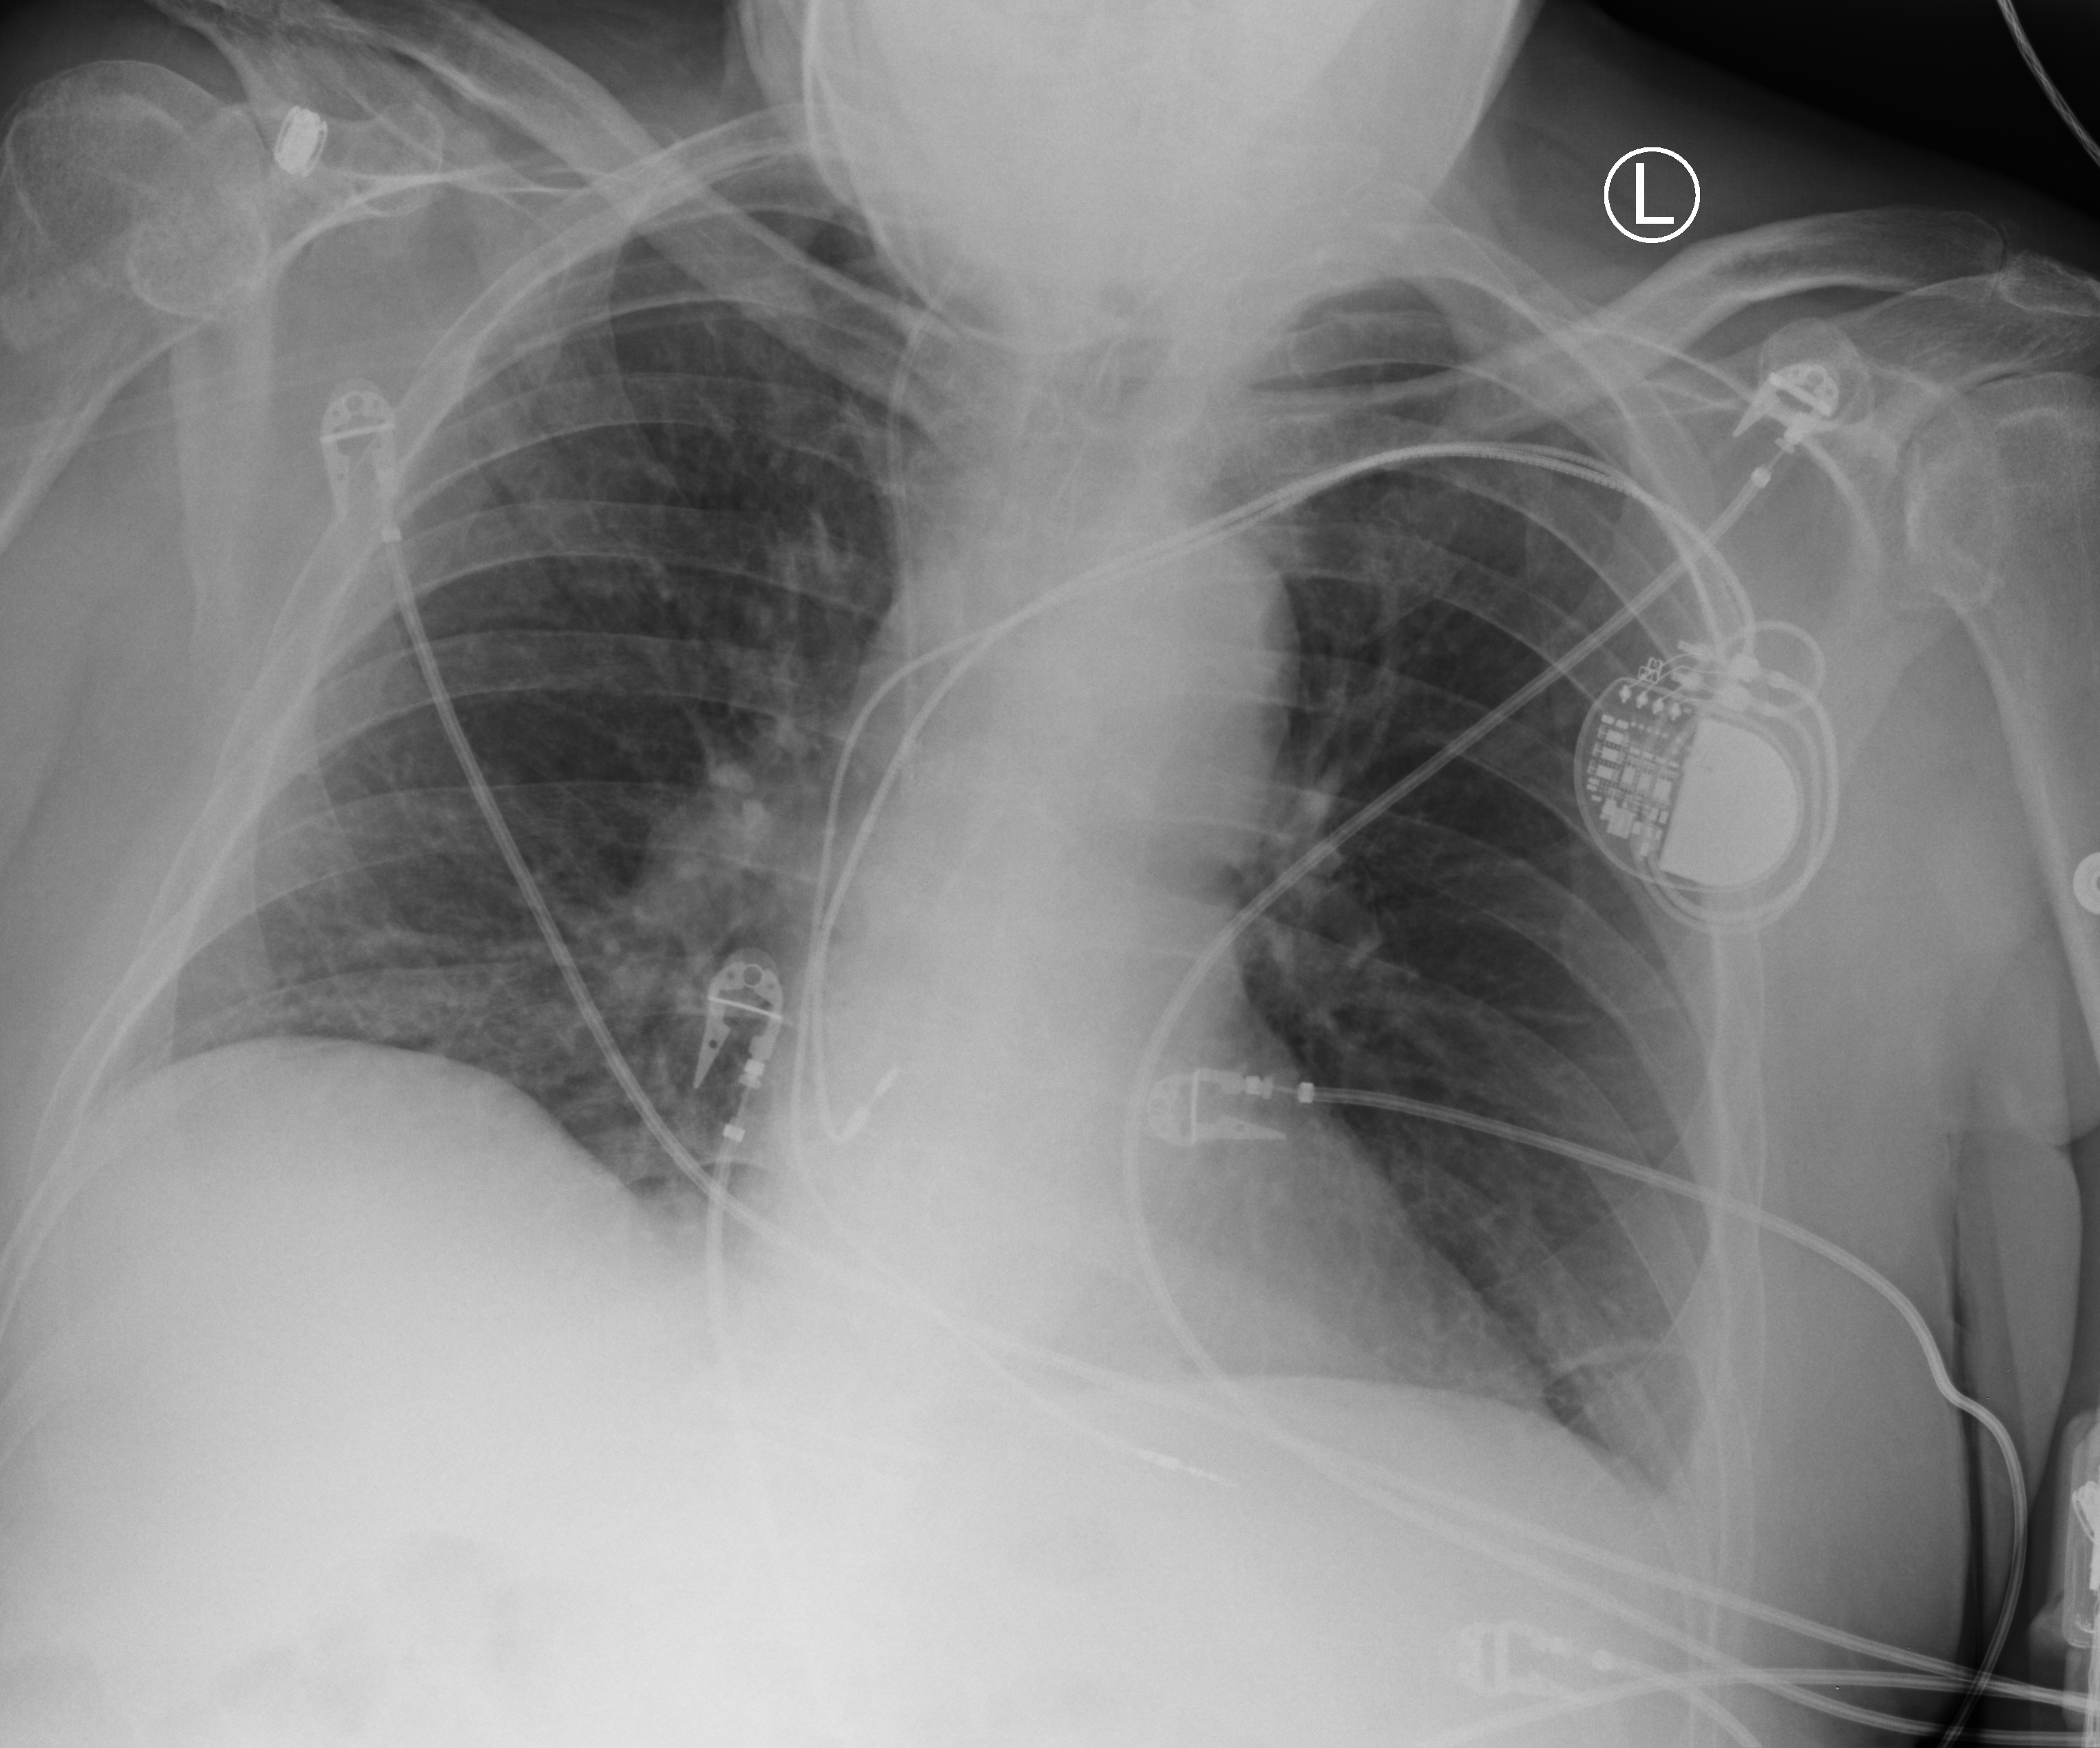
Portable chest radiograph, anteroposterior (AP) projection. Male patient hospitalised with COVID-19, age 60–74 years.
Admission-level facts for this patient (not findings on this image; timing relative to this image not recorded): admitted to intensive care during this hospital stay: no; mechanically ventilated during this hospital stay: no; diabetes (admission record): no.